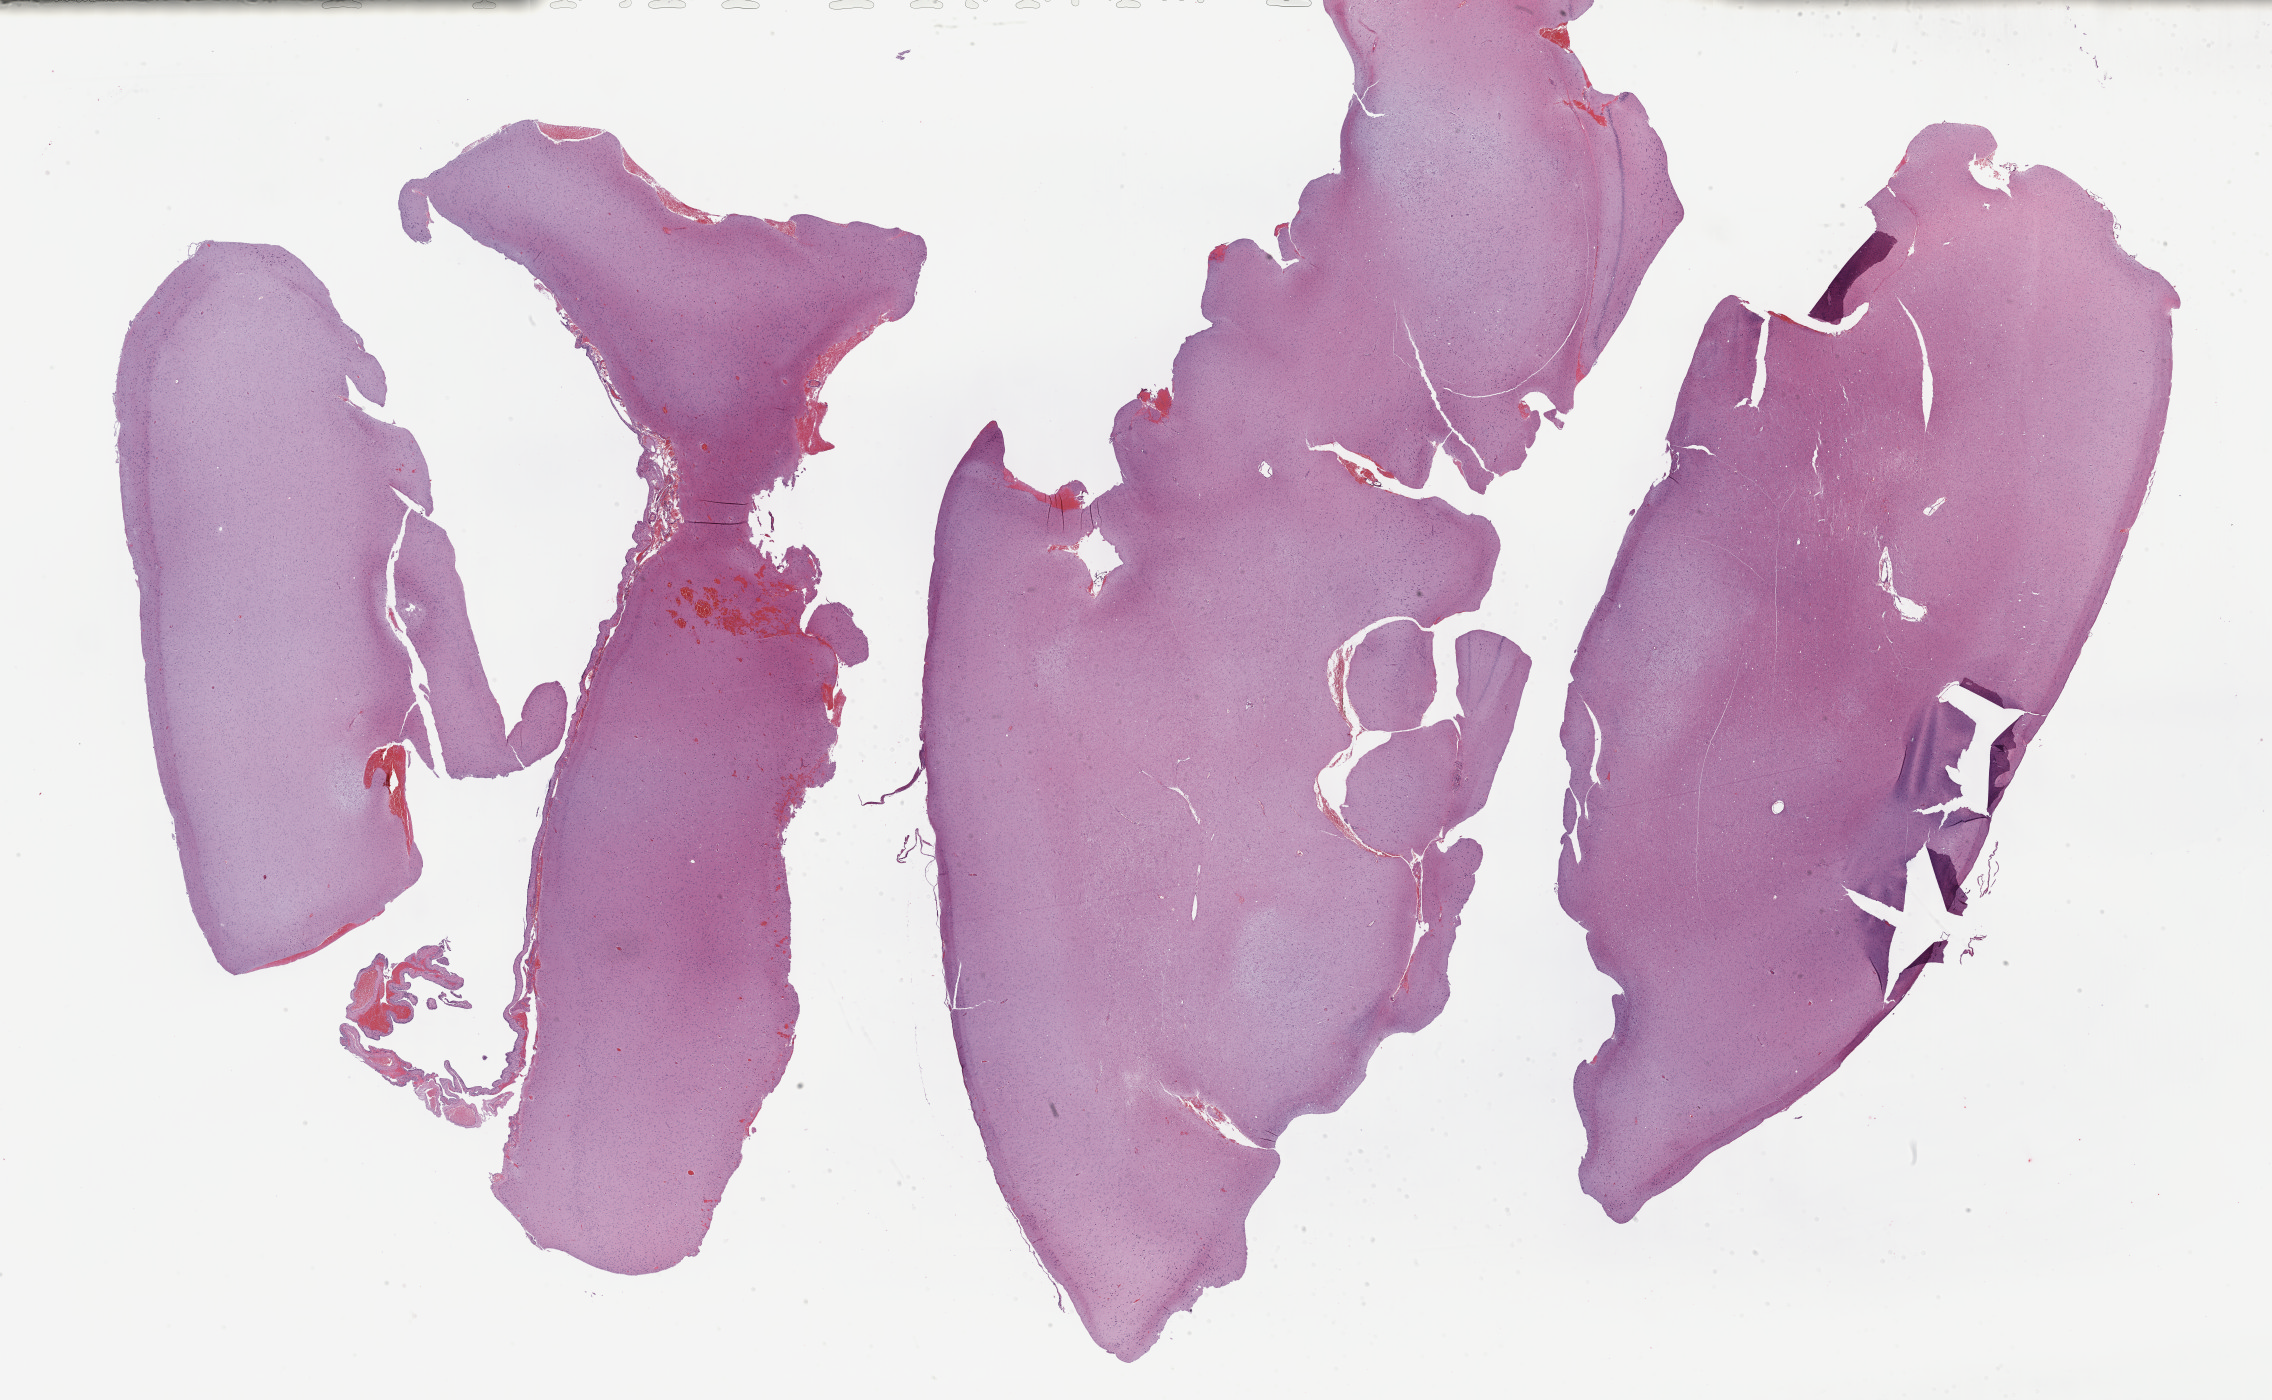
Hematoxylin and eosin (H&E) stained whole-slide image — shown as a low-resolution overview of the whole scanned area (about 36.7 x 22.6 mm, acquisition: 40x scan); FFPE section; brain, primary tumour sample. Patient: female, age at initial diagnosis 37 years. Histologic grade: G2 (moderately differentiated).
Diagnosis: Astrocytoma, NOS (cerebrum).